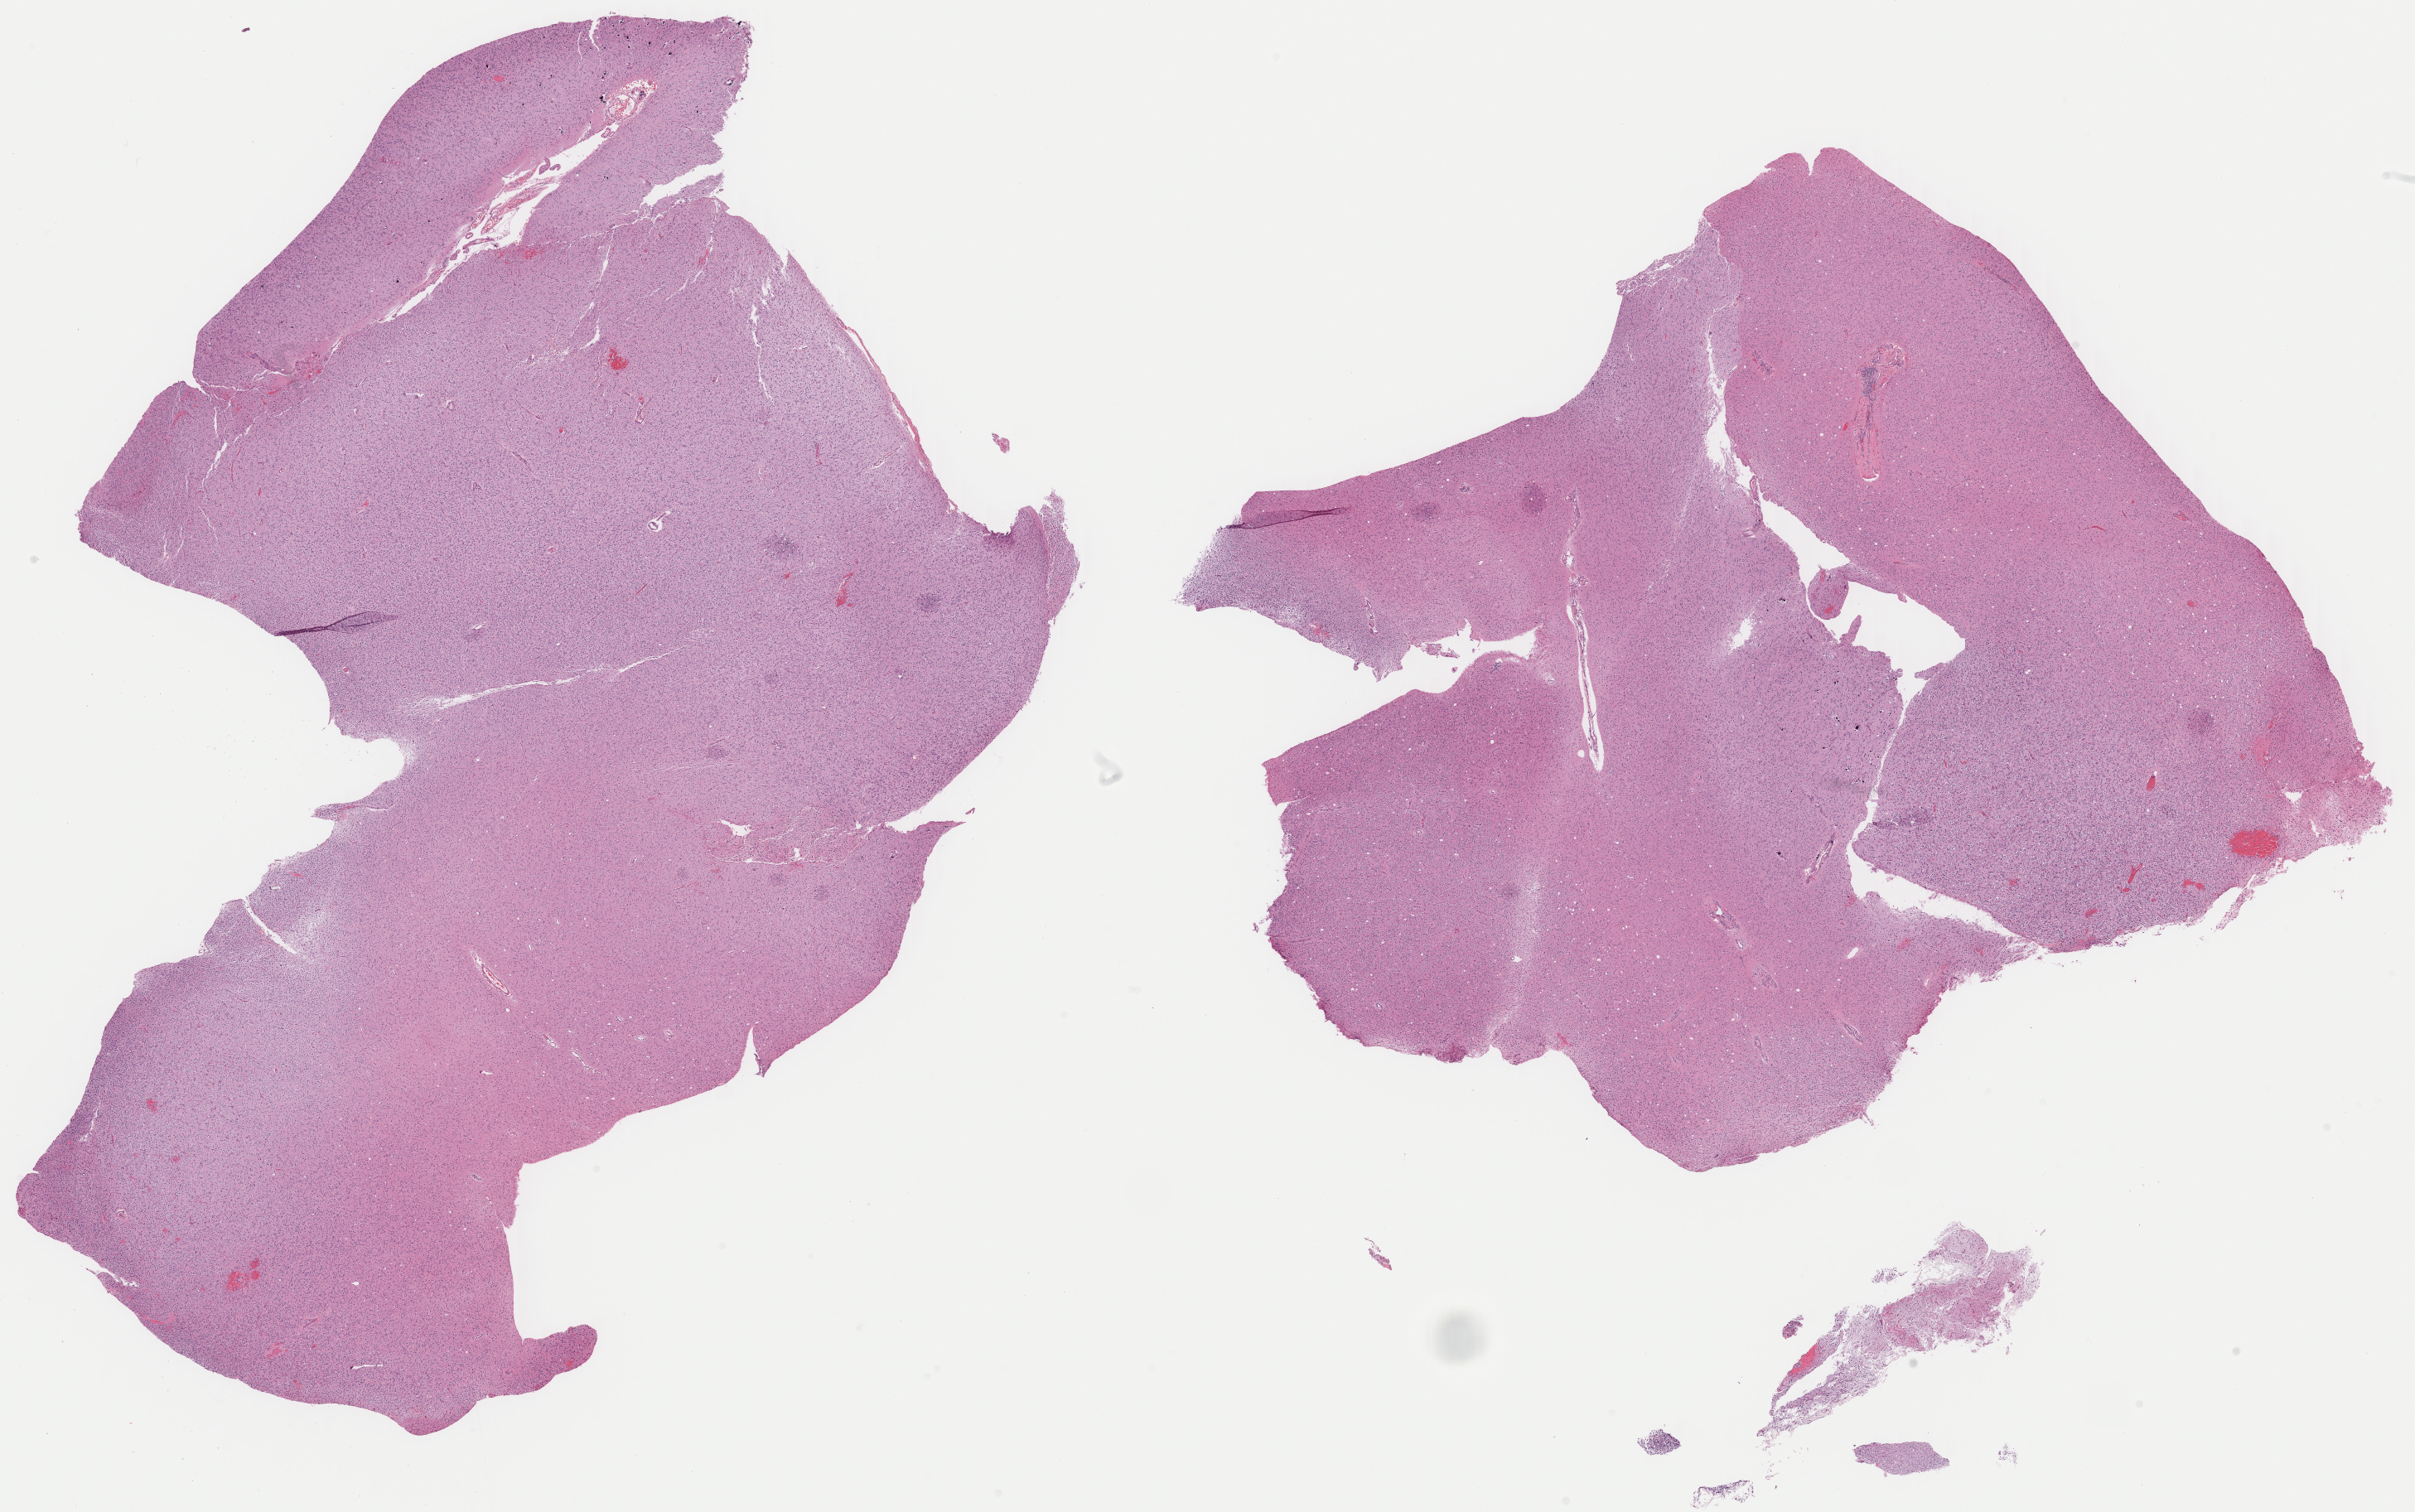
Hematoxylin and eosin (H&E) stained whole-slide image, shown as a low-resolution overview of the whole scanned area (about 23.0 x 14.4 mm, acquisition: 40x scan), formalin-fixed paraffin-embedded (FFPE) diagnostic section, brain, primary tumour sample. Male patient; age at initial diagnosis 30 years. Histologic grade: G2 (moderately differentiated).
Pathologic diagnosis: Mixed glioma (temporal lobe).